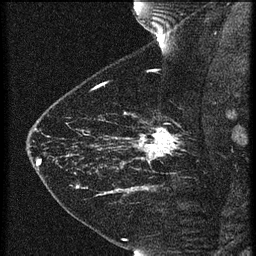
Breast MRI (dynamic contrast-enhanced), one sagittal slice. Slice 49 of 60 in the series (ordered by position). 3 images stored at this slice position (order not interpretable as contrast timing). 1.5 T. TE 4.2 ms, TR 21.3 ms. 1.5 mm slice thickness. 256 × 256 image matrix, field of view 180 × 180 mm. Female patient, age 43 years. Case-level facts recorded for this patient, not image findings: setting: breast cancer imaged before/during neoadjuvant chemotherapy; receptor status: HER2-positive.
Annotated regions visible in this slice (semi-automatic segmentation, software-assisted and operator-edited):
- analysis volume of interest (the breast-tissue region the enhancement analysis was run in; not a lesion): bounding box [x1, y1, x2, y2] px = [119, 114, 189, 173]
- tumour enhancement mask (voxels above the 90 % enhancement threshold inside the analysis volume of interest): [134, 128, 180, 161]